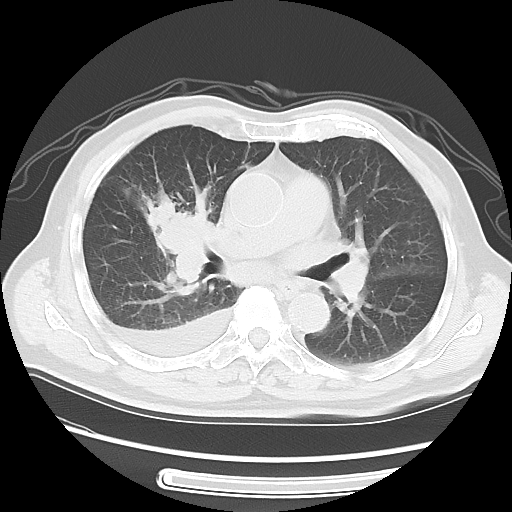
Chest CT, one axial slice. Lung window (W 1500 / L -600 HU). 5 mm slice thickness. 512 × 512 image matrix, field of view 360 × 360 mm. Patient: male, 77 years. Case-level facts recorded for this patient, not image findings: clinical TNM (as recorded): T3 N3 M1b.
Outlined on this slice (rectangle marked by the reading radiologist):
- lung tumour (recorded histology: small cell carcinoma): box from (x=131, y=194) to (x=219, y=292) px